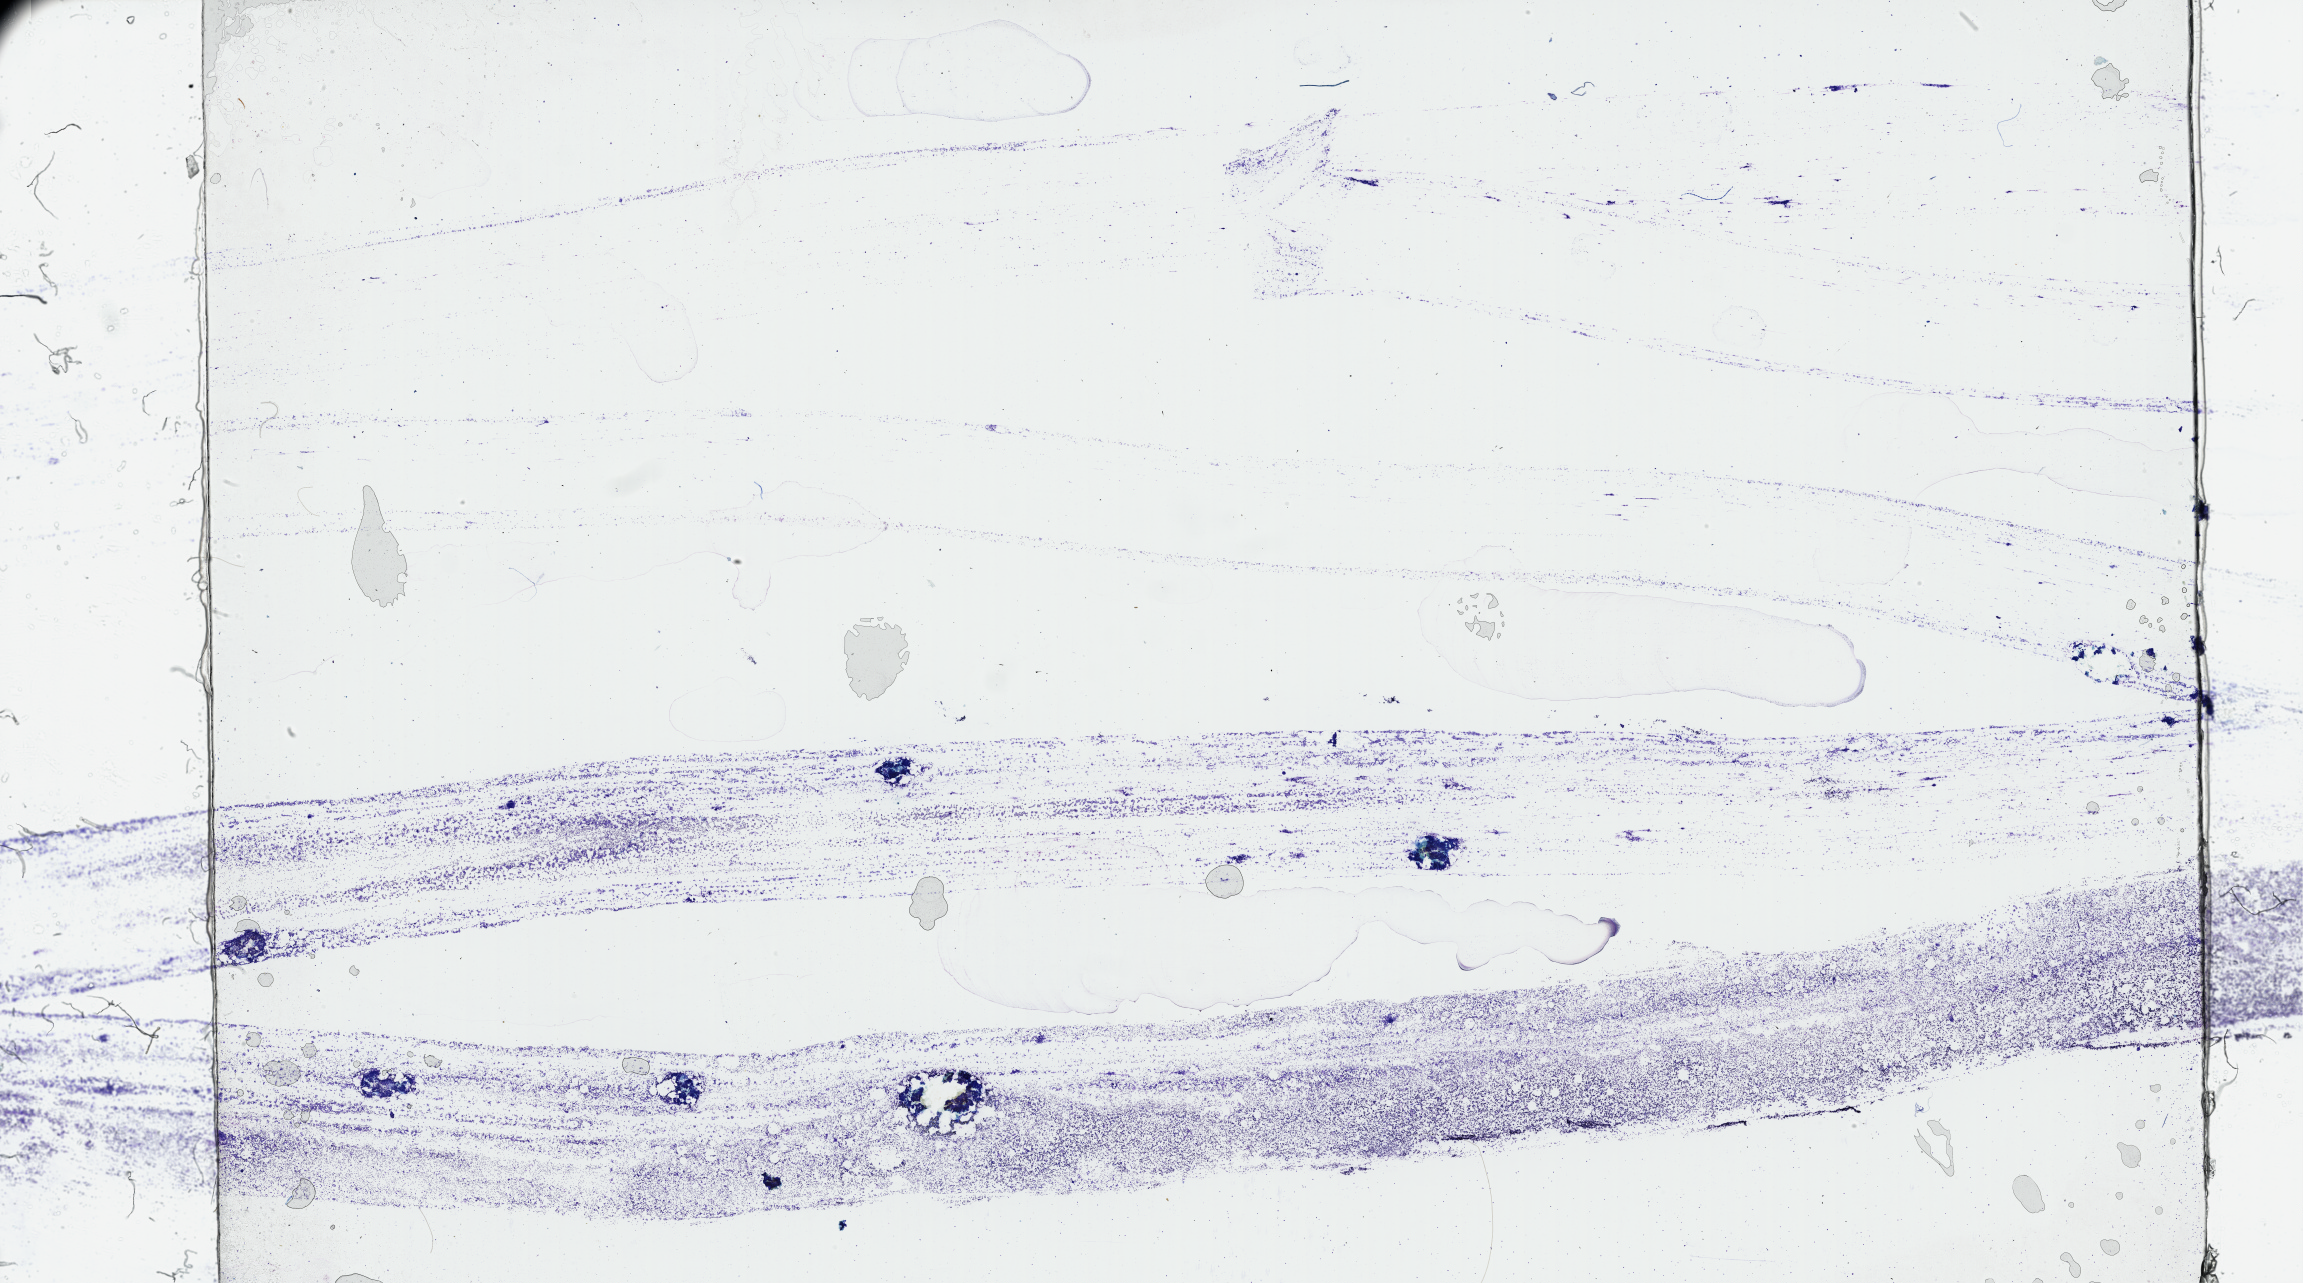
Digitized H&E tissue section (whole slide) — a low-resolution overview of the entire scanned area, about 37.2 x 20.7 mm (from a 40x scan). Bone marrow (leukaemic) sample. 76-year-old female patient. Blasts: 70%.
Diagnosis: Acute Myeloid Leukemia. FAB classification: M4.